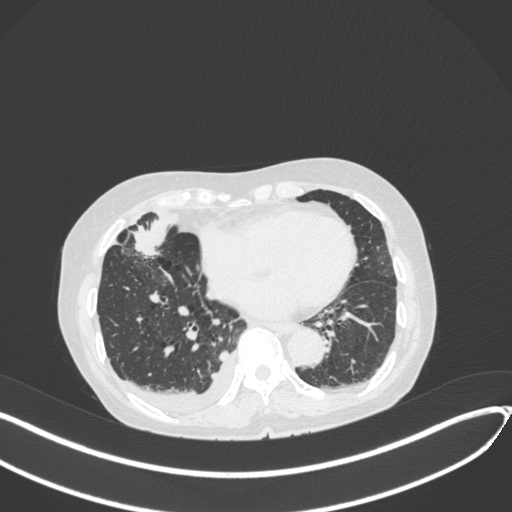
Chest CT, one axial slice. Position 137 of 418 along the scan axis. Lung window (W 1500 / L -600 HU). 512 × 512 image matrix. Female patient, age 75 years. From the clinical record (not read from this slice): clinical TNM (as recorded): T2a N3 M0.
Structures marked on this image (rectangle marked by the reading radiologist):
- lung tumour (recorded histology: adenocarcinoma): bounding box (x1, y1, x2, y2) in pixels: (132, 218, 174, 261)